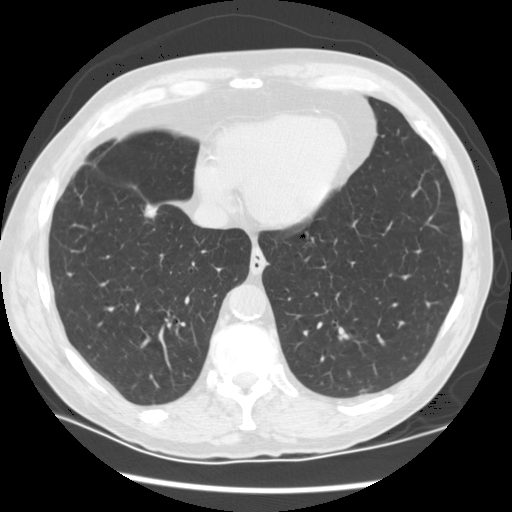
Chest CT (low-dose screening protocol), one axial image. Baseline screening round. Lung window (W 1500 / L -600 HU). 2.5 mm slice thickness. 512 × 512 image matrix. Male participant, aged 68 years at enrolment. Current smoker at enrolment.
Lesion marked by an expert reader, bounding box (x1, y1, x2, y2) in pixels: (122, 188, 184, 237). The screening reader recorded 3 non-calcified nodules or masses ≥4 mm on this exam (right upper lobe, right upper lobe, right lower lobe); which of them this box marks is not recorded.